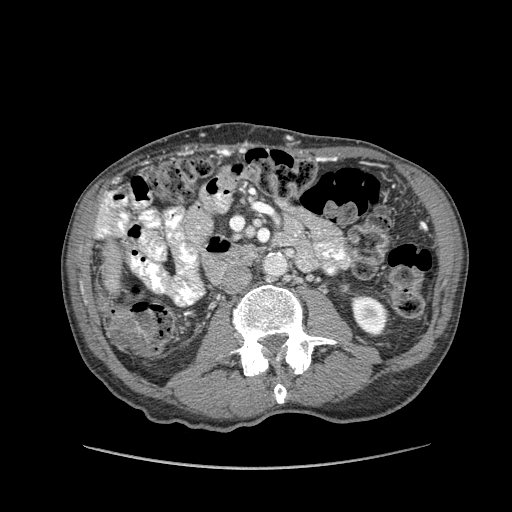
Contrast-enhanced abdominal CT (liver protocol), one axial slice; position 9 of 162 along the scan axis; reconstruction kernel STANDARD; 100 kVp; soft-tissue window (W 400 / L 40 HU); 2.5 mm slice thickness; 512 × 512 image matrix. From the clinical record (not read from this slice): diagnosis: hepatocellular carcinoma (patient treated with transarterial chemoembolisation; whether this scan precedes or follows treatment is not stated here); TNM stage (as recorded): Stage-IIIA; Child-Pugh class: A; tumour nodularity: multinodular; tumour size: 9.9 cm.
Structures marked on this image (semi-automatically segmented with operator editing):
- liver parenchyma outside the tumour (the mass and vessels are separate outlines, so this box may not span the whole liver): bounding box [x1, y1, x2, y2] px = [94, 192, 127, 350]
- liver vessels: [98, 194, 113, 237]